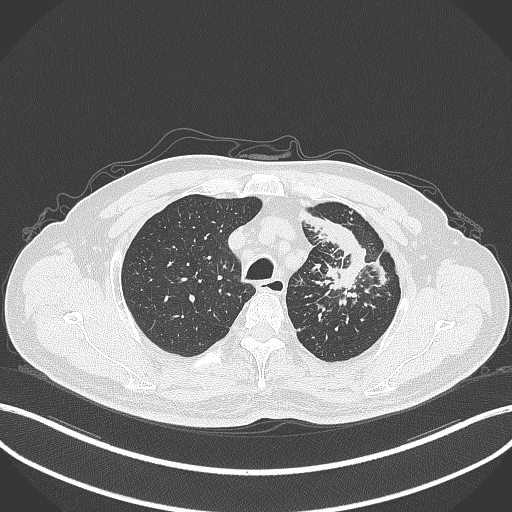
Chest CT, one axial slice; slice 287 of 386 in the series (ordered by position); 120 kVp; lung window (W 1500 / L -600 HU); 512 × 512 image matrix, field of view 400 × 400 mm. Male patient, age 69 years. From the clinical record (not read from this slice): clinical TNM (as recorded): T2a N2 M0; histopathological grade: G2-3.
Outlined on this slice (bounding box drawn by a radiologist):
- lung tumour (recorded histology: adenocarcinoma): bounding box [x1, y1, x2, y2] px = [302, 211, 368, 296]